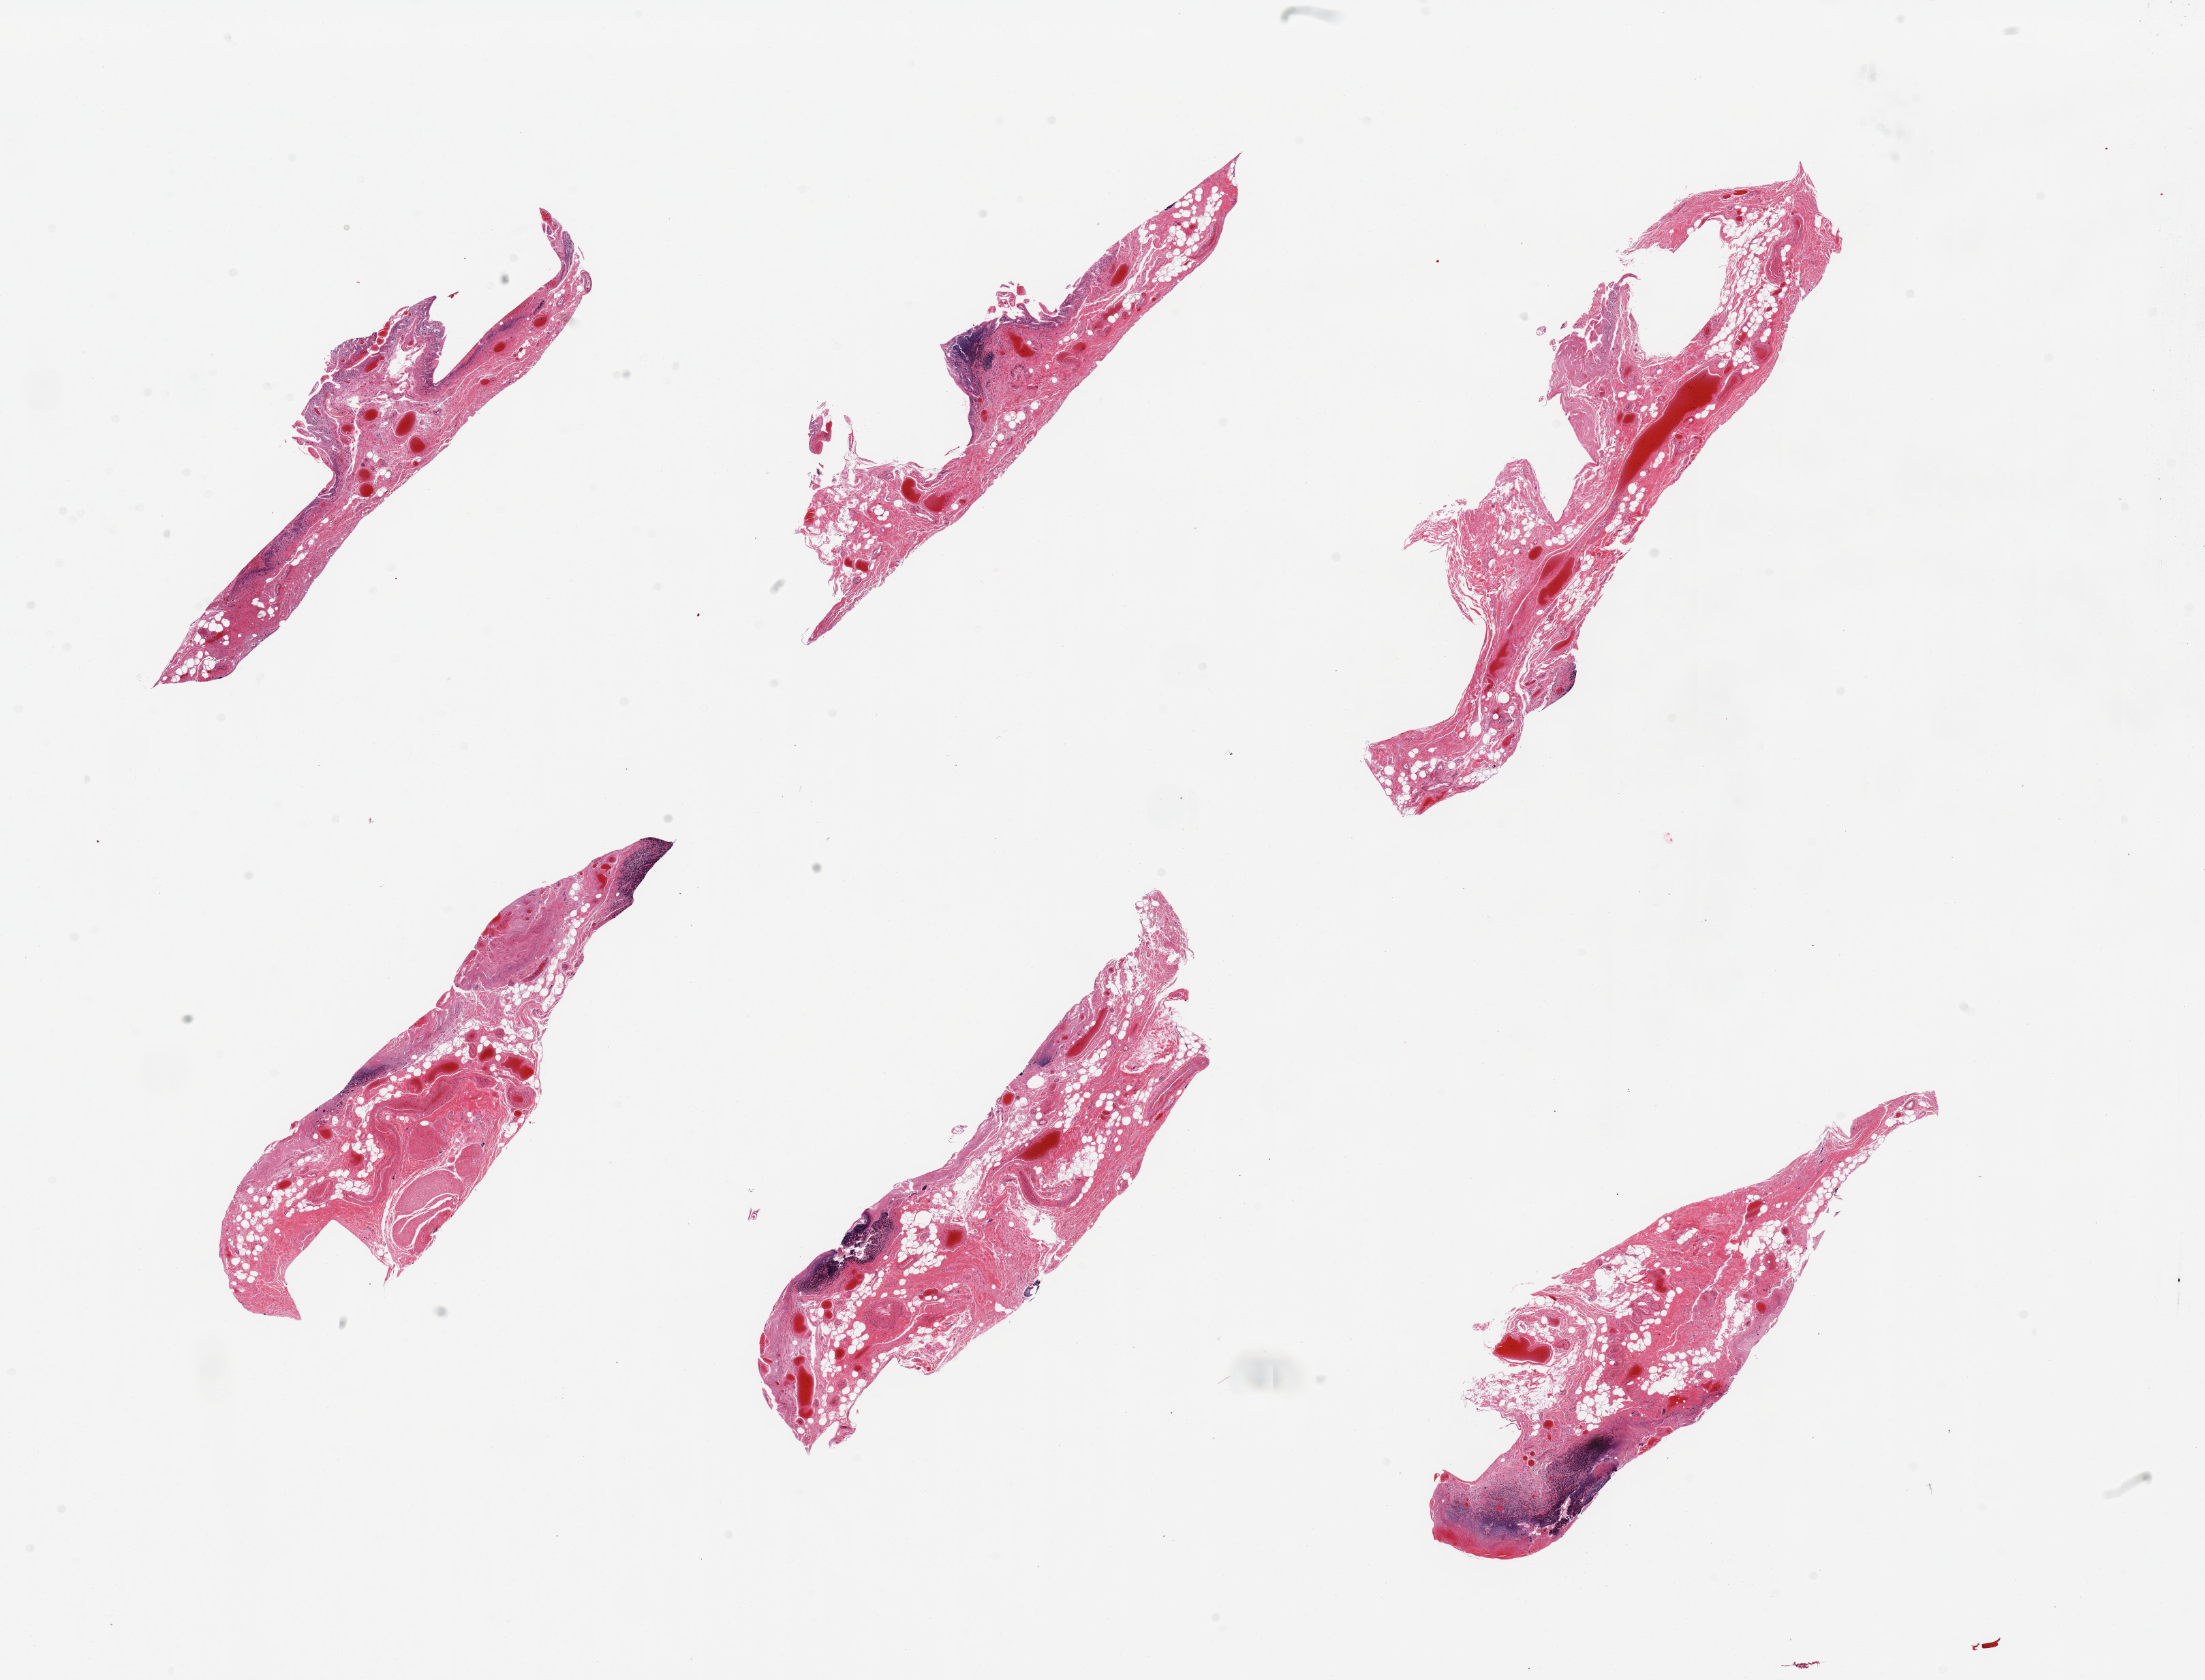
Hematoxylin and eosin (H&E) whole-slide image, shown as a low-resolution overview of the whole scanned area (about 25.6 x 19.5 mm).
* specimen: PAXgene-fixed paraffin-embedded (PFPE) section; section of ileum (target tissue); tissue donor sample